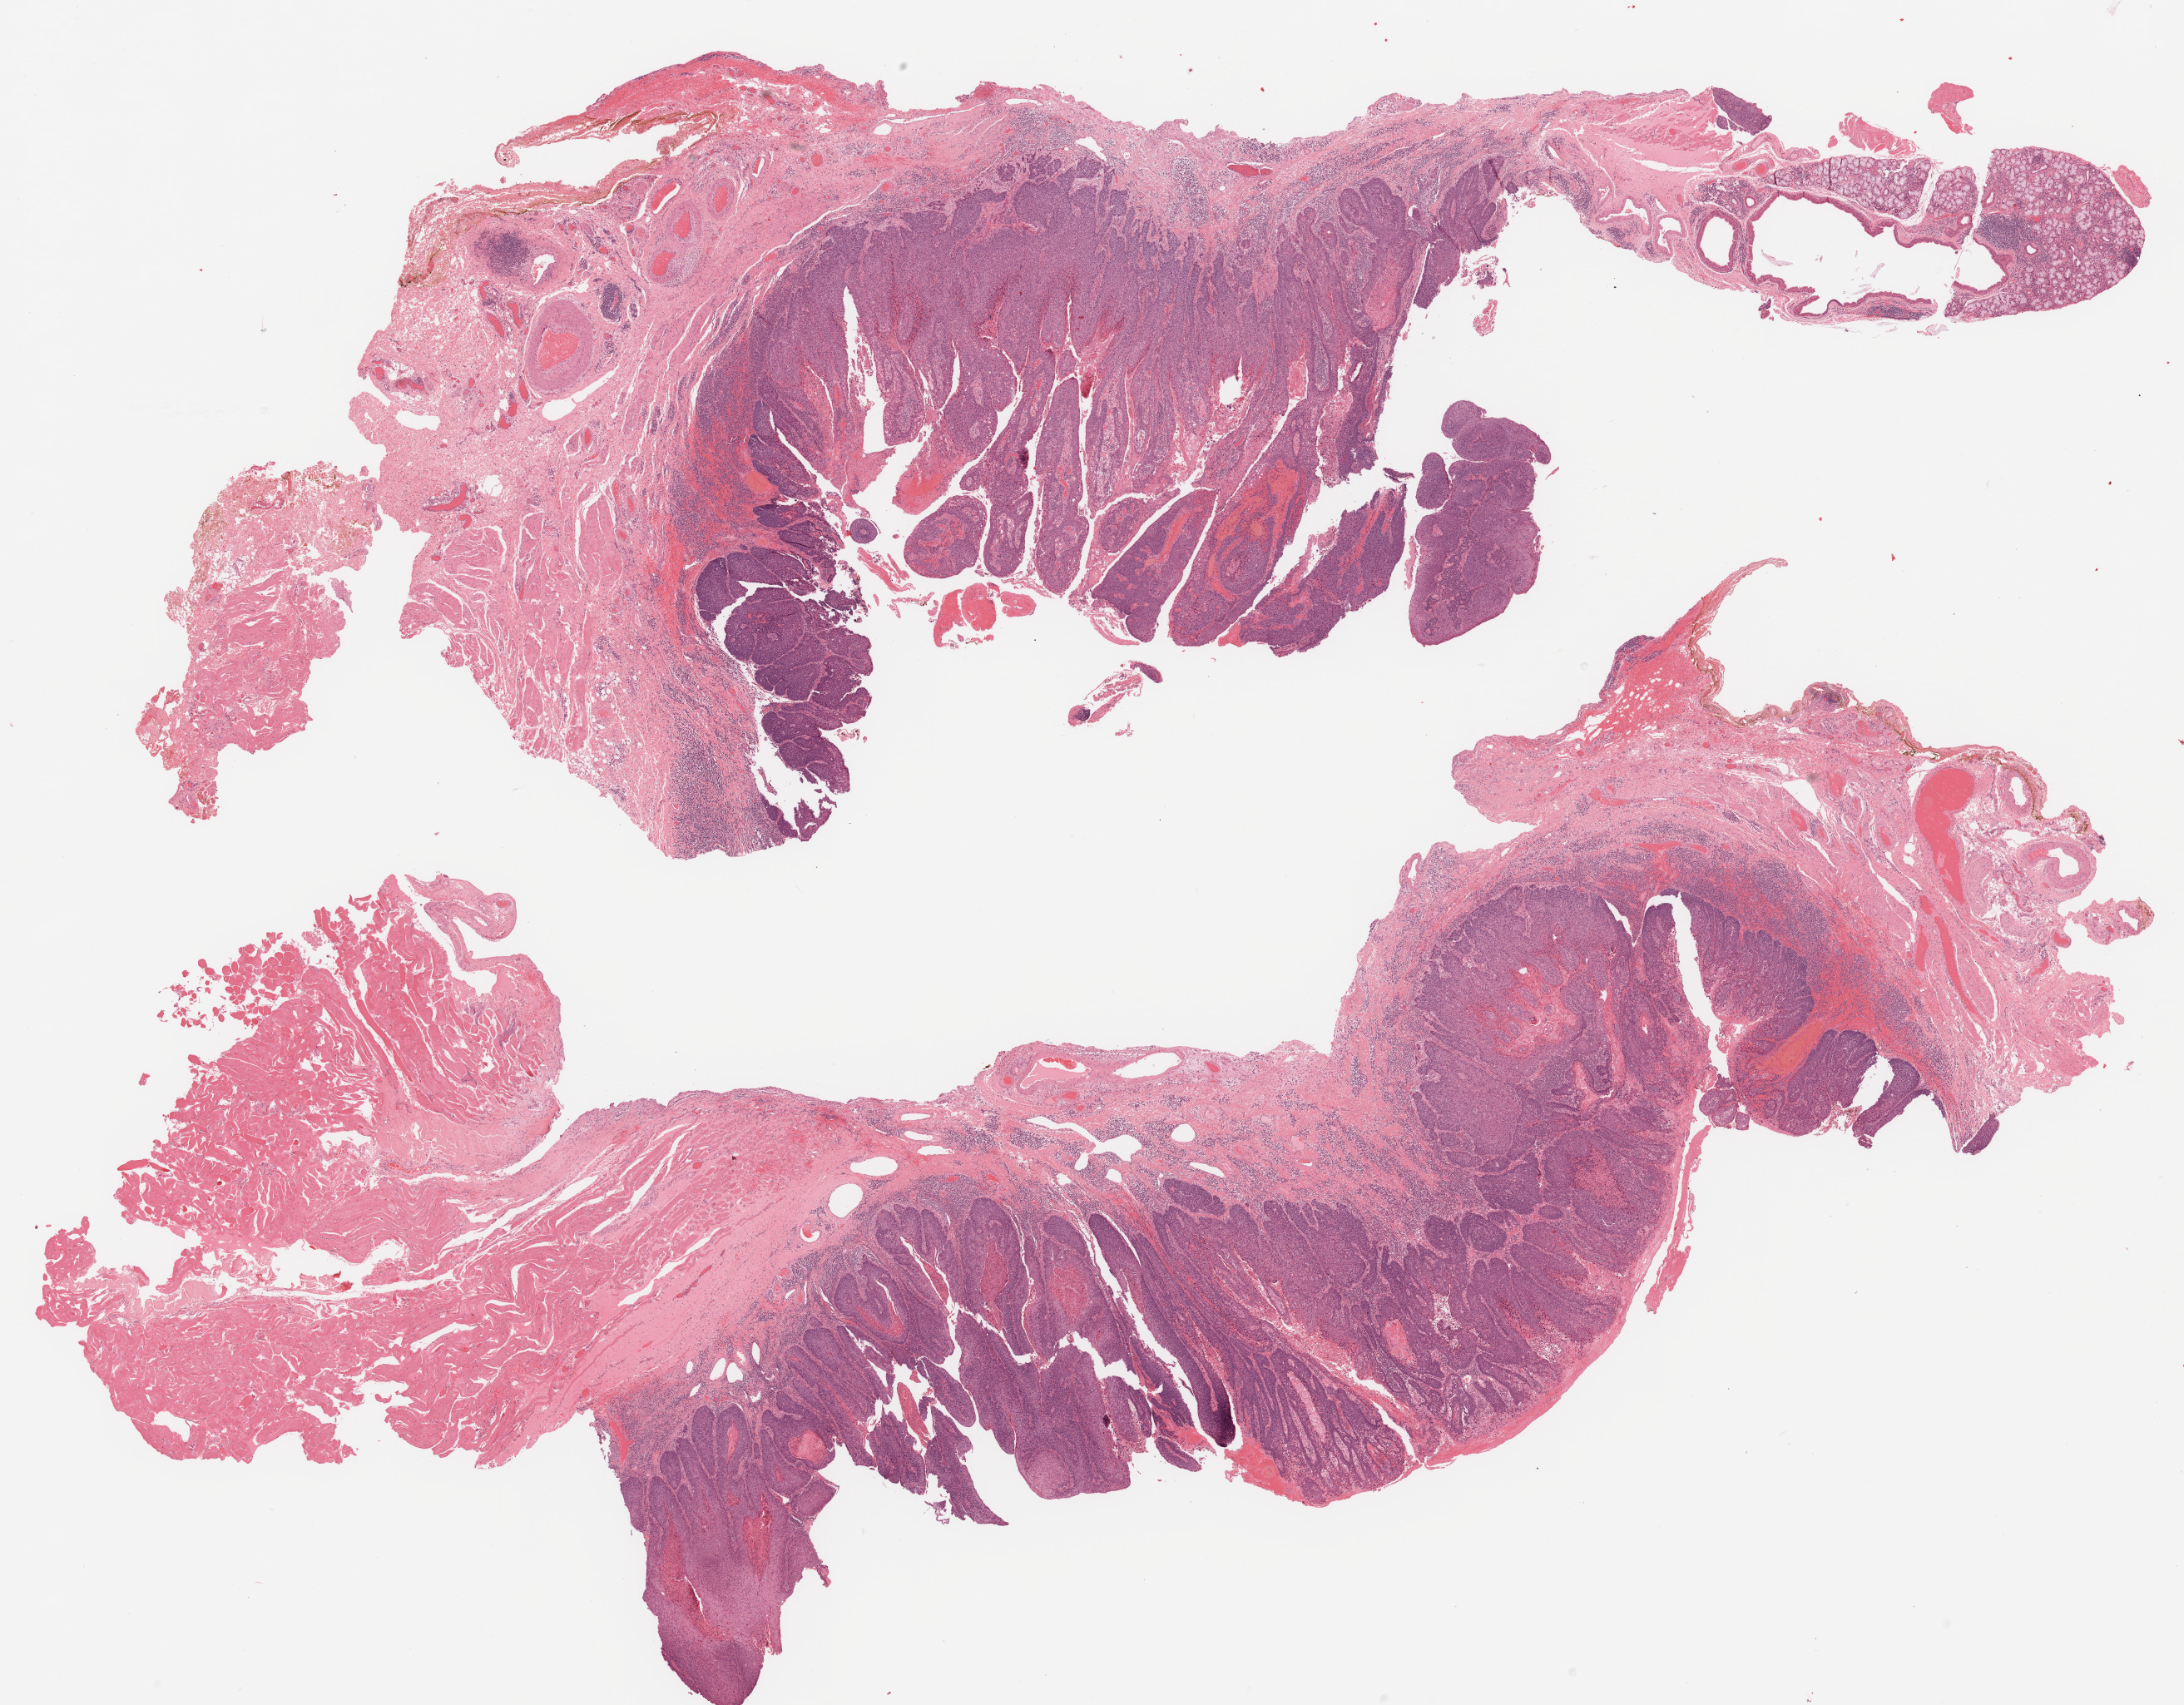
H&E whole-slide image, shown as a low-resolution overview of the whole scanned area (about 21.1 x 16.4 mm, slide scanned at 20x), formalin-fixed paraffin-embedded (FFPE) diagnostic section, sample: primary tumour, head and neck. Patient: male, age at initial diagnosis 82 years. Histologic grade: G2 (moderately differentiated).
* AJCC pathologic stage: I
* TNM: T1 N0
* histologic diagnosis: Squamous cell carcinoma, NOS (overlapping lesion of lip, oral cavity and pharynx)